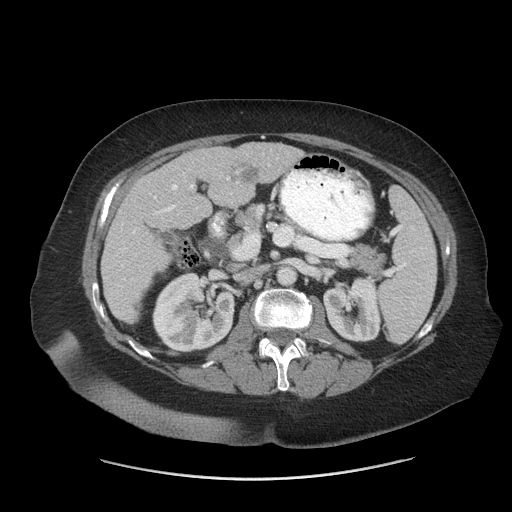
Contrast-enhanced abdominal CT (liver protocol), one axial slice. Slice 27 of 69 in the series (ordered by position). 140 kVp. Soft-tissue window (W 400 / L 40 HU). 512 × 512 image matrix. From the clinical record (not read from this slice): diagnosis: hepatocellular carcinoma (patient treated with transarterial chemoembolisation; whether this scan precedes or follows treatment is not stated here); TNM stage (as recorded): Stage-IIIB; Child-Pugh class: A; tumour differentiation: moderately differentiated; tumour nodularity: multinodular.
Annotated regions visible in this slice (semi-automatic segmentation, software-assisted and operator-edited):
- liver parenchyma outside the tumour (the mass and vessels are separate outlines, so this box may not span the whole liver): bounding box [x1, y1, x2, y2] px = [100, 142, 304, 323]
- liver vessels: [122, 177, 229, 280]